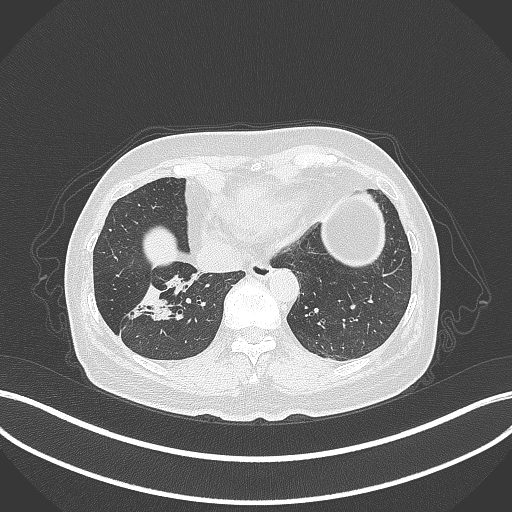
Chest CT, one axial slice; slice 108 of 429 in the series (ordered by position); reconstruction kernel B70f; lung window (W 1500 / L -600 HU); 512 × 512 image matrix, field of view 400 × 400 mm. Female patient, age 67 years. From the clinical record (not read from this slice): clinical TNM (as recorded): T1c N1 M0.
Structures marked on this image (bounding box drawn by a radiologist):
- lung tumour (recorded histology: adenocarcinoma): bounding box [x1, y1, x2, y2] px = [134, 276, 194, 322]